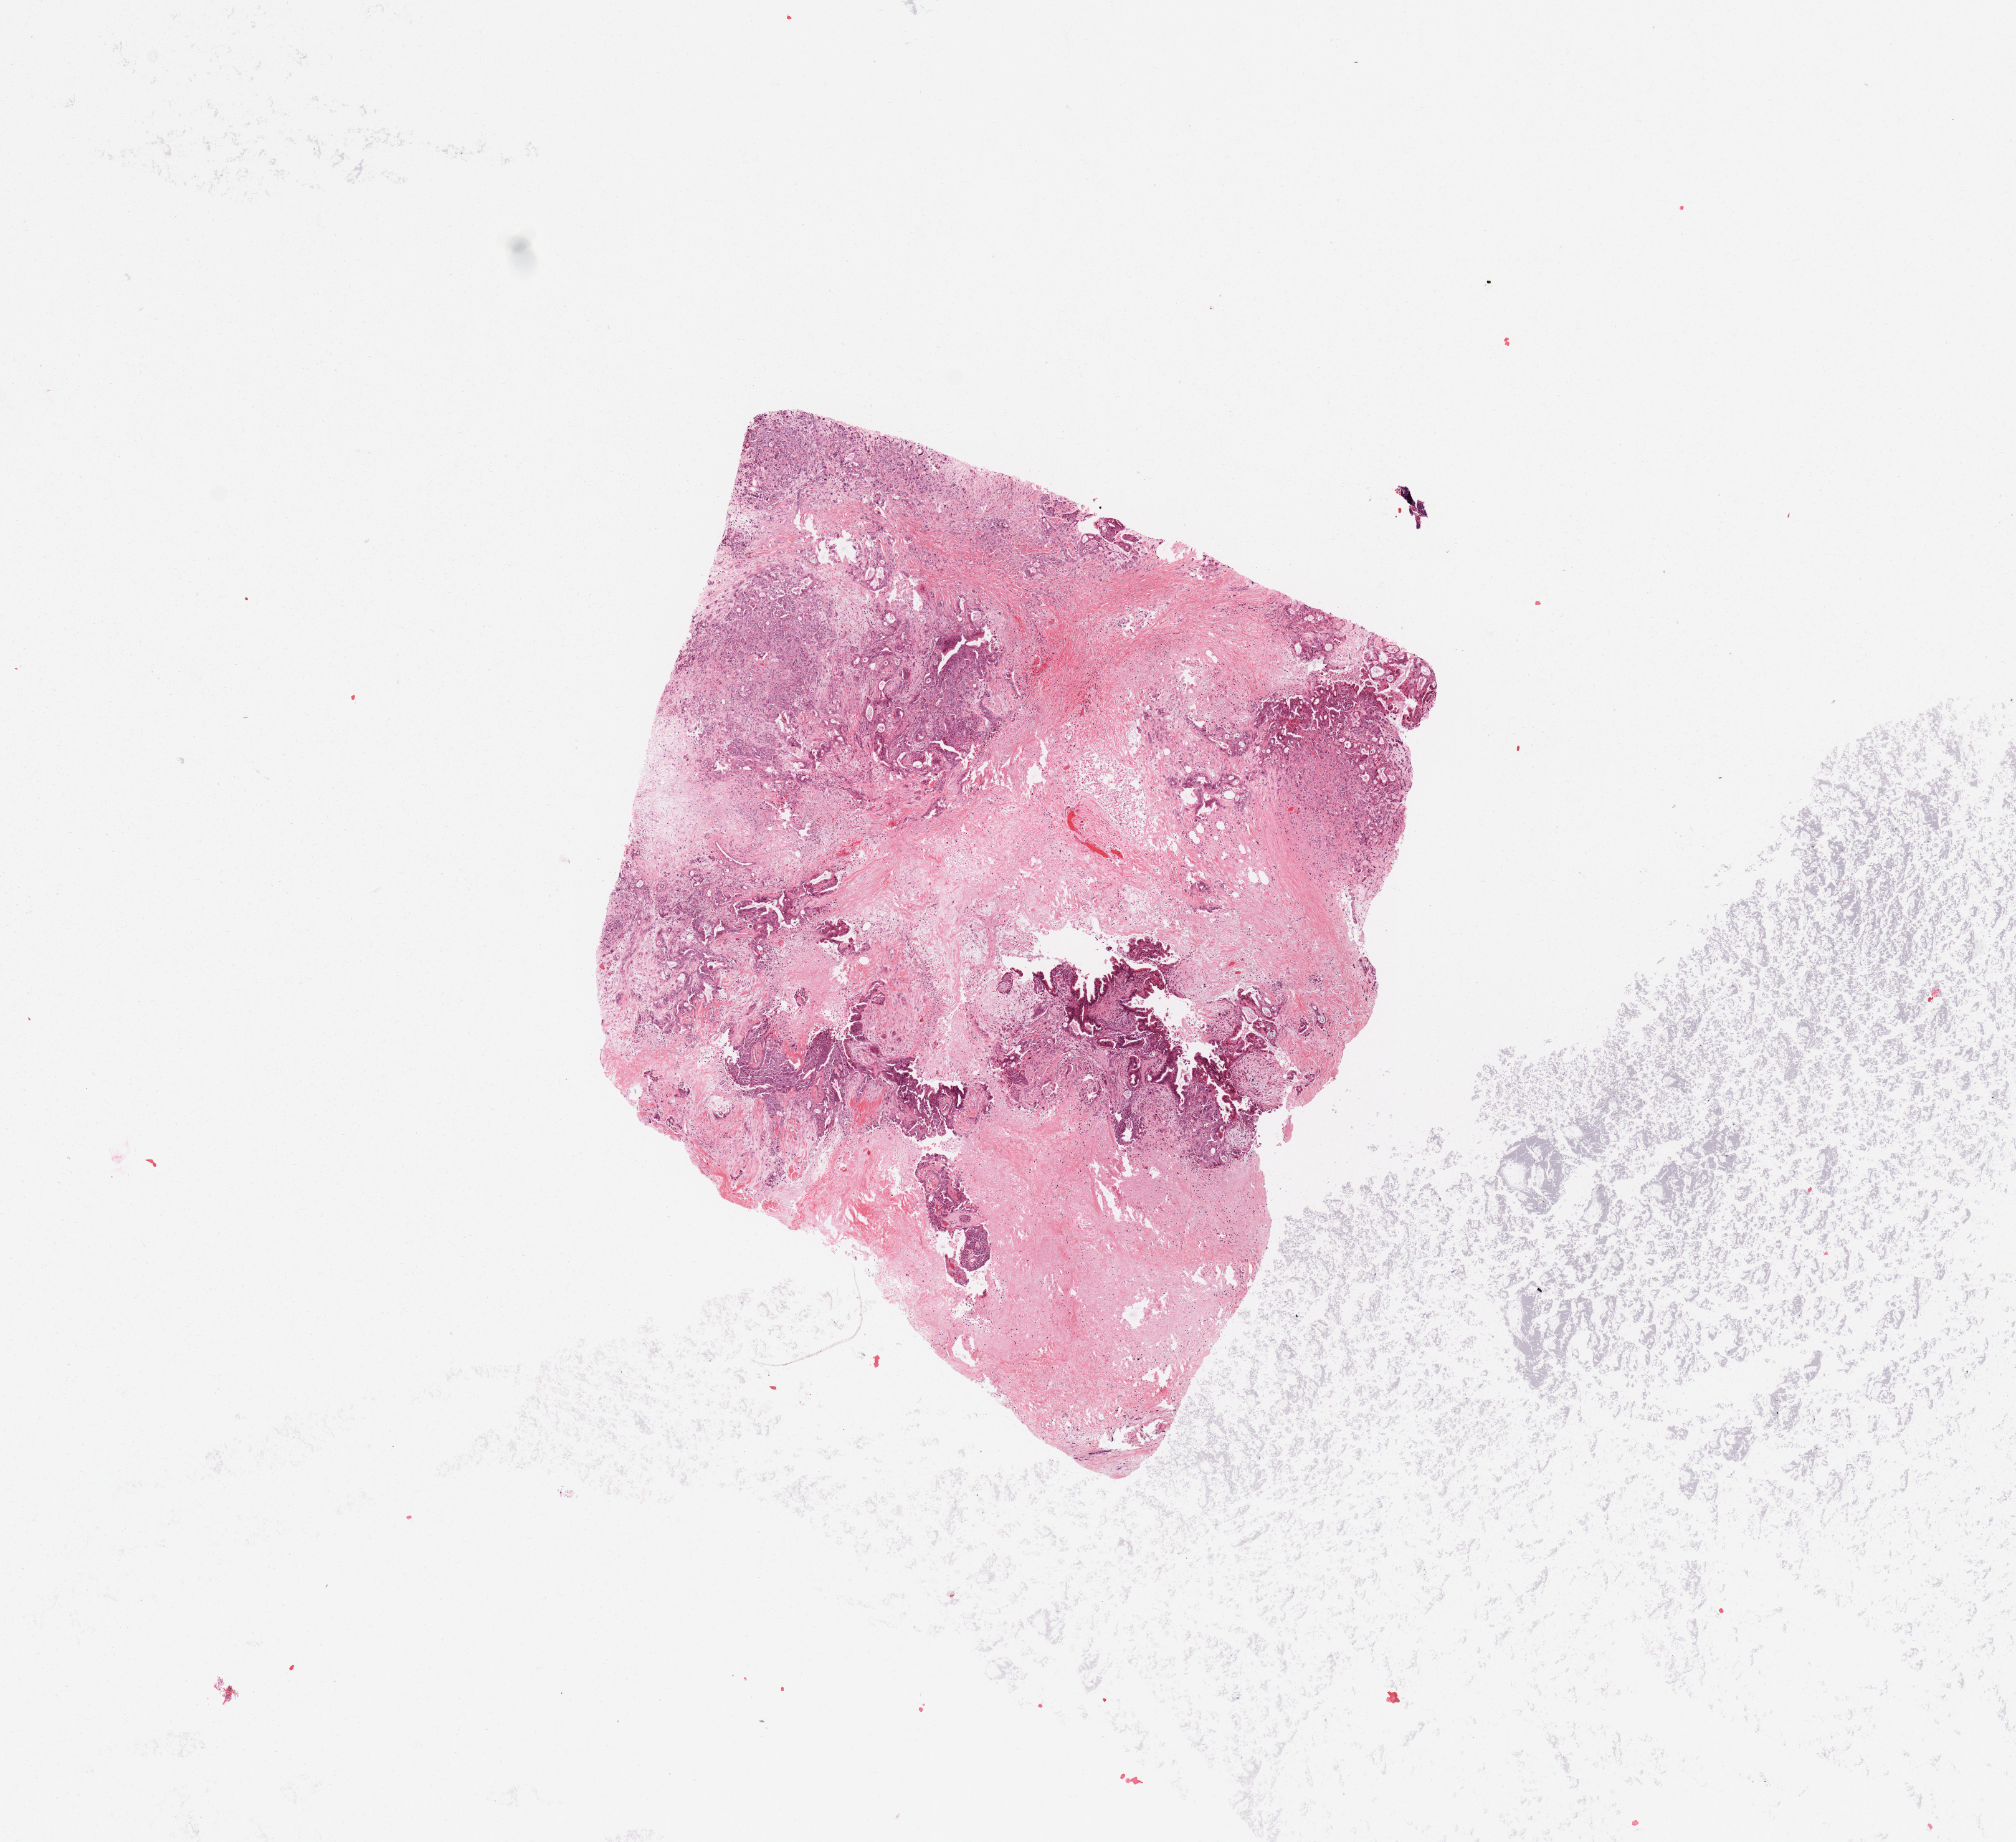
Digitized Hematoxylin and eosin (H&E) stained tissue section (whole slide), a low-resolution overview of the entire scanned area, about 12.8 x 11.7 mm; tumour tissue sample, sampled site: pancreas. Patient: male, age 46 years. Histologic grade: G3 (poorly differentiated). Pathologist review of this section (percent, as recorded): tumour nuclei 40%, necrosis 20%.
* diagnosis: Infiltrating duct carcinoma, NOS
* AJCC pathologic stage: IIB